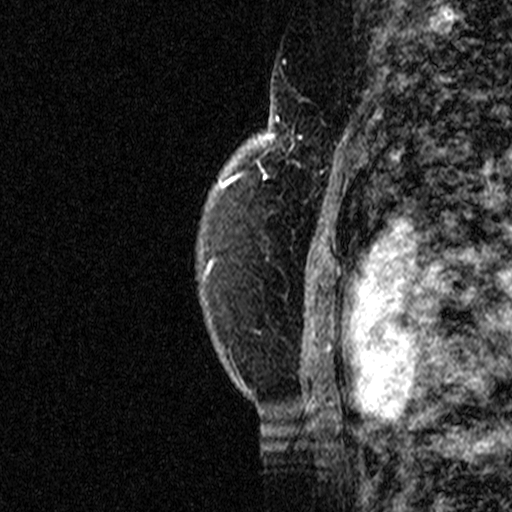
Breast MRI (dynamic contrast-enhanced), one sagittal slice. Position 33 of 44 along the scan axis. Dynamic contrast-enhanced study with each time point stored as its own series, time point 2 of 3 at this slice position (early post-contrast, ordered by acquisition time). 1.5 T. TE 4.5 ms, TR 11 ms. 3 mm slice thickness. 512 × 512 image matrix. Patient: female, 49 years. From the clinical record (not read from this slice): setting: breast cancer imaged before/during neoadjuvant chemotherapy; receptor status: triple-negative.
Structures marked on this image (semi-automatic segmentation, software-assisted and operator-edited):
- analysis volume of interest (the breast-tissue region the enhancement analysis was run in; not a lesion): bounding box <254,112,347,207> (left, top, right, bottom; pixels)
- tumour enhancement mask (voxels above the 90 % enhancement threshold inside the analysis volume of interest): <255,120,346,206>